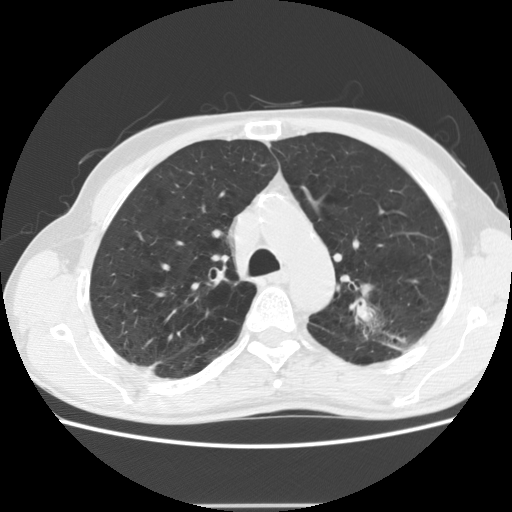
Low-dose screening chest CT, one axial slice. Position 139 of 191 along the scan axis. 120 kVp. Lung window (W 1500 / L -600 HU). 512 × 512 image matrix.
Annotated regions visible in this slice (manually delineated by an expert):
- lesion 1 (tumor, upper lobe of left lung): bounding box [x1, y1, x2, y2] px = [355, 302, 374, 324]